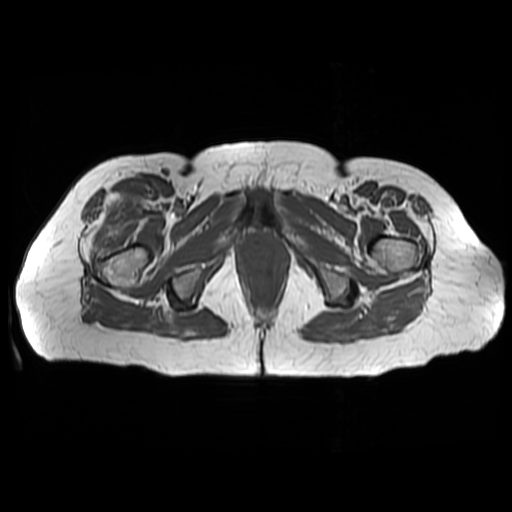
MRI of an extremity soft-tissue mass, one axial slice. Position 40 of 48 along the scan axis. 512 × 512 image matrix. Female patient. From the clinical record (not read from this slice): histological type: pleiomorphic undifferentiated sarcoma; grade: high; site of the primary tumour: right quadricep.
Annotated regions visible in this slice (outlined manually by an expert reader):
- gross tumour volume including surrounding oedema: box from (x=87, y=191) to (x=154, y=259) px